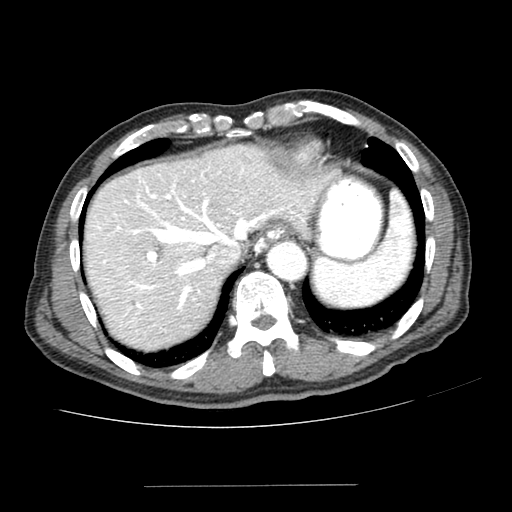
Contrast-enhanced abdominal CT (liver protocol), one axial slice; position 170 of 187 along the scan axis; reconstruction kernel SOFT; 100 kVp; one of 2 acquisitions stored at this slice position; soft-tissue window (W 400 / L 40 HU); 2.5 mm slice thickness; 512 × 512 image matrix, field of view 360 × 360 mm. From the clinical record (not read from this slice): diagnosis: hepatocellular carcinoma (patient treated with transarterial chemoembolisation; whether this scan precedes or follows treatment is not stated here); TNM stage (as recorded): Stage-I; Child-Pugh class: A; tumour differentiation: poorly differentiated; tumour nodularity: uninodular.
Outlined on this slice (semi-automatically segmented with operator editing):
- liver parenchyma outside the tumour (the mass and vessels are separate outlines, so this box may not span the whole liver): bounding box [x1, y1, x2, y2] px = [85, 144, 324, 350]
- mass: [129, 251, 156, 283]
- liver vessels: [96, 168, 314, 319]